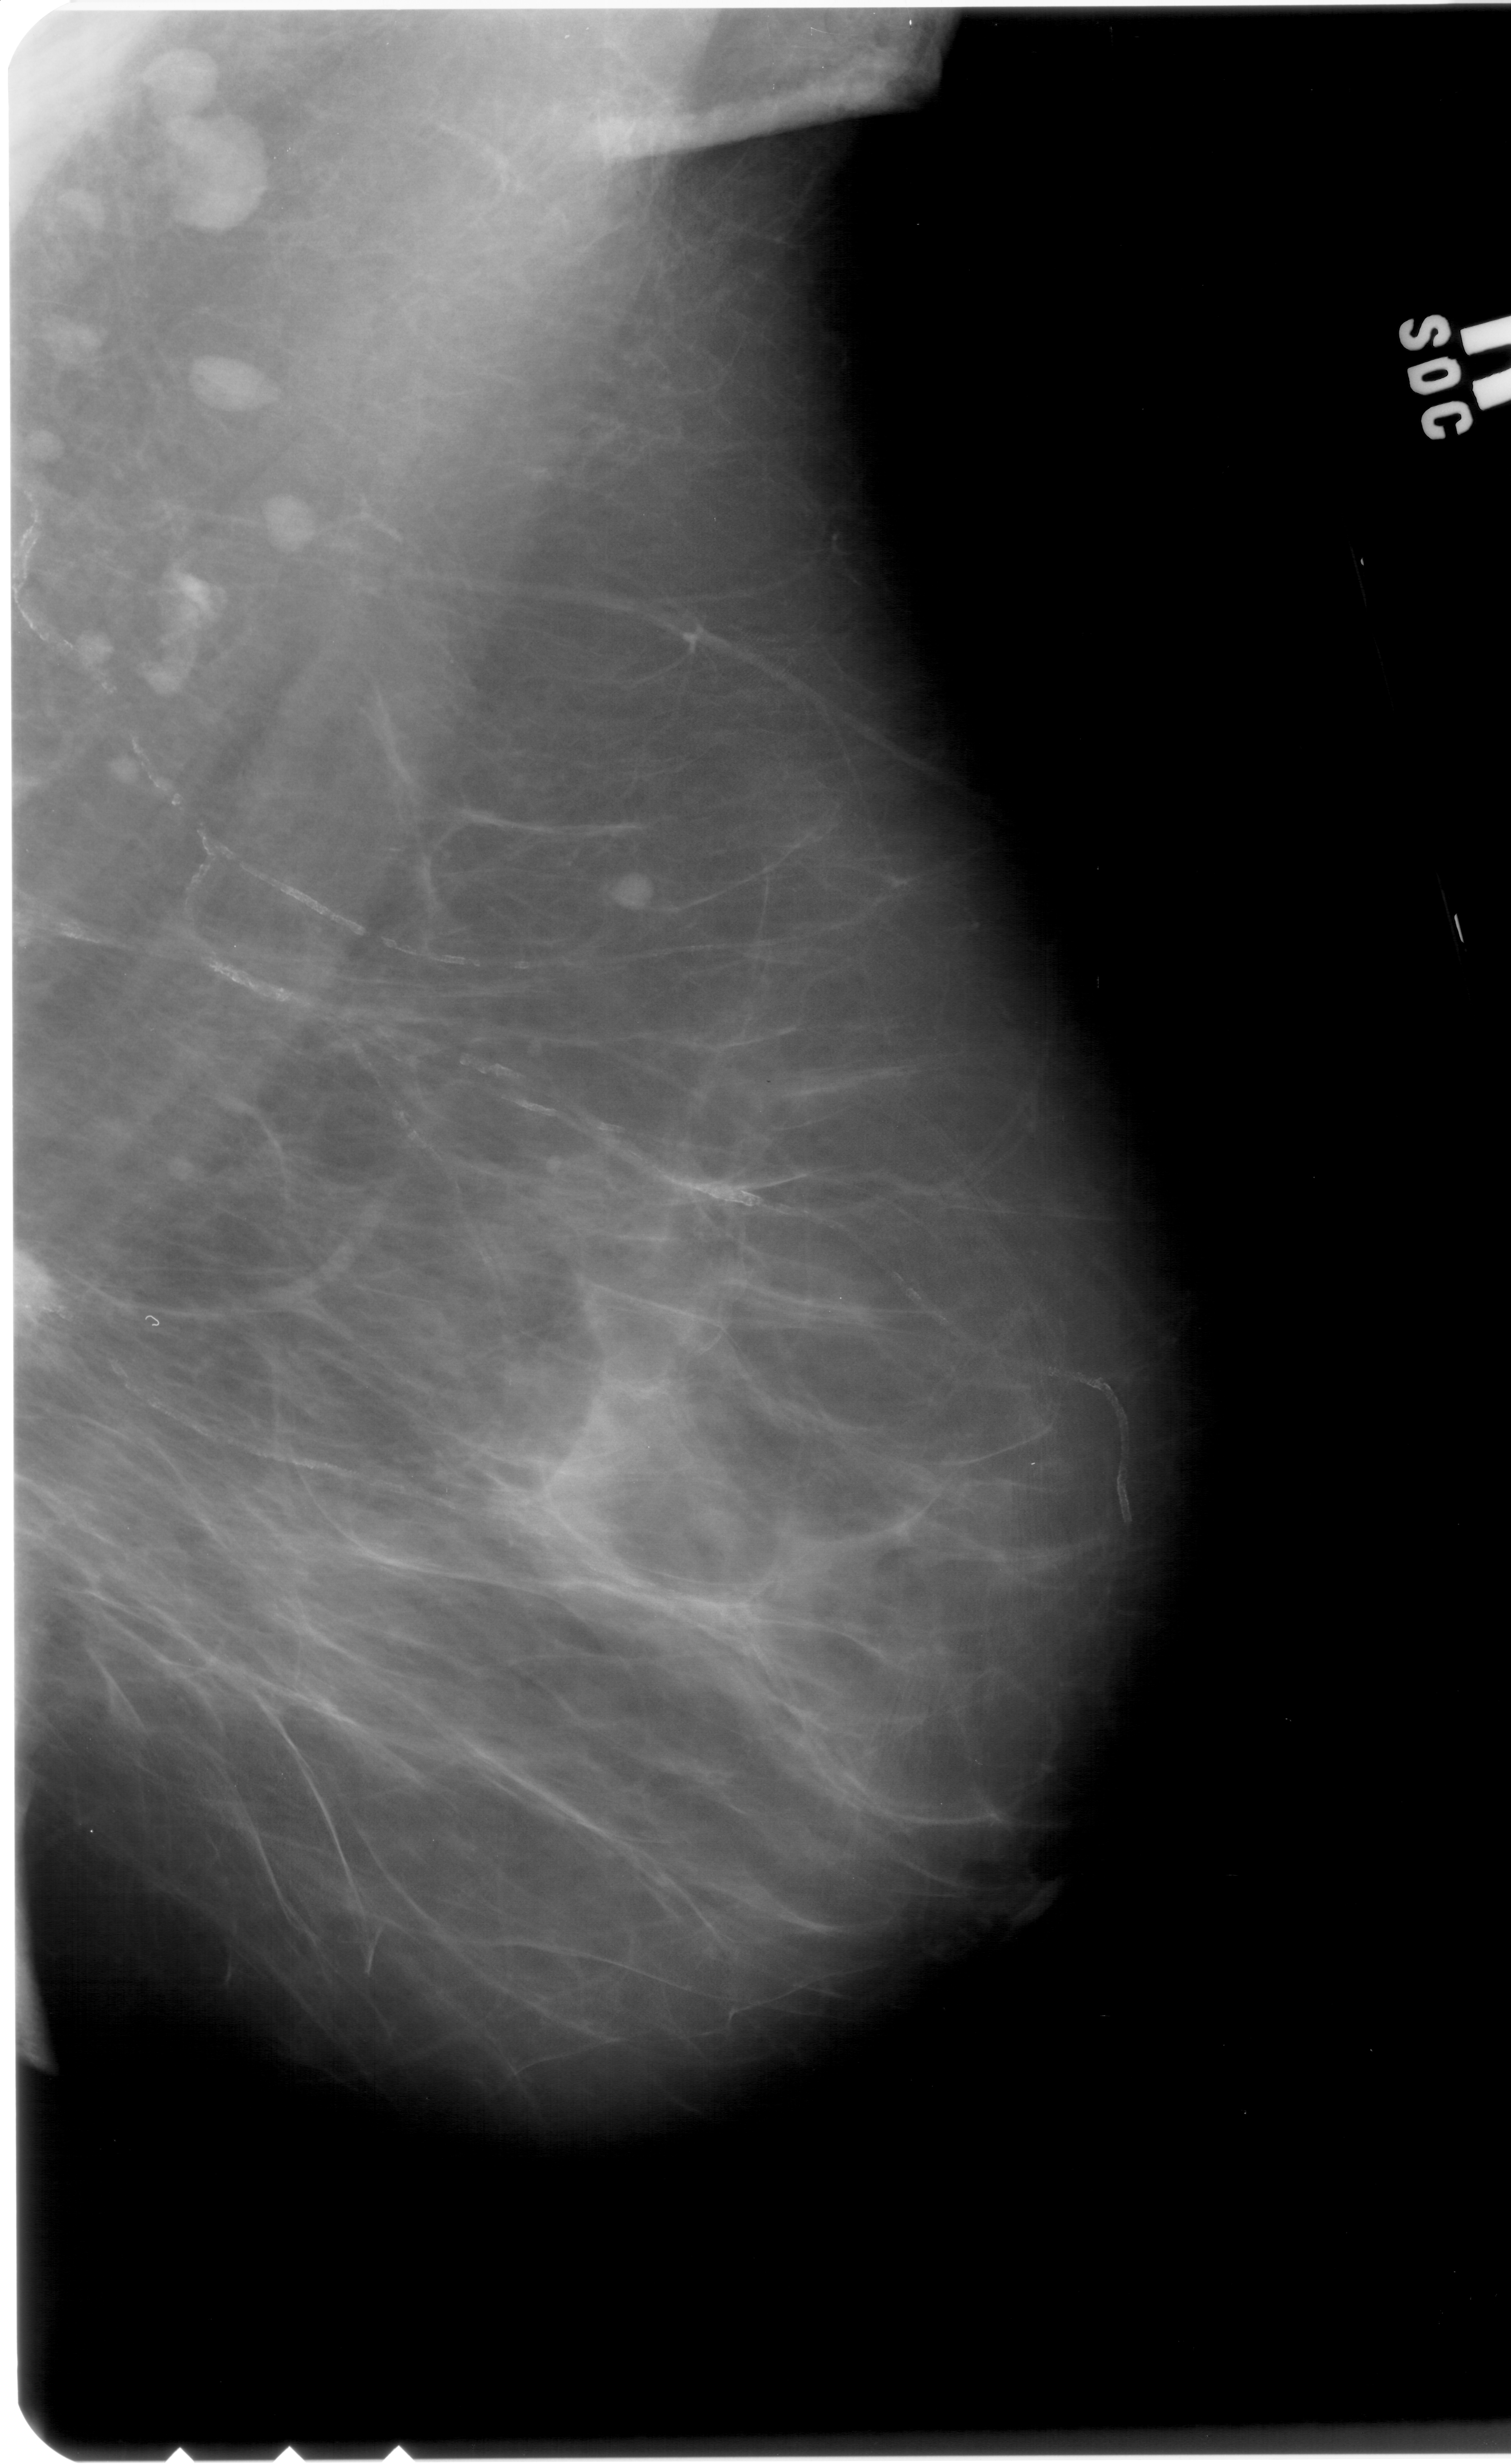
Mammogram (digitized film); right breast; mediolateral oblique (MLO) view; breast composition: extremely dense (BI-RADS density category 4 of 4); 1511 × 2464 image matrix.
Marked abnormalities (boxes around the expert regions of interest):
- mass, shape irregular, margins ill defined; BI-RADS assessment category 4; pathology result (as recorded, not read from the image): malignant: bounding box (x1, y1, x2, y2) in pixels: (6, 1253, 58, 1332)